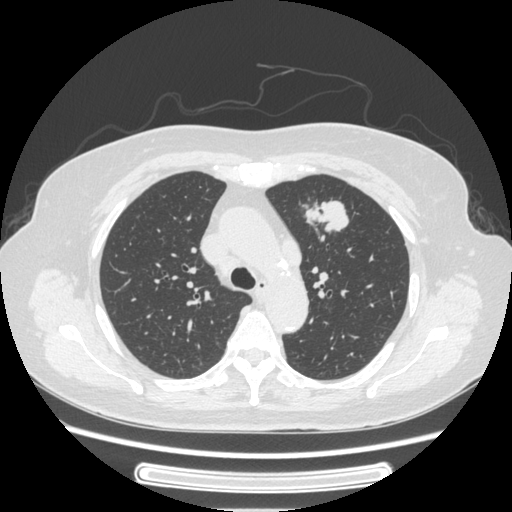
Chest CT, one axial slice. Slice 170 of 227 in the series (ordered by position). Lung window (W 1500 / L -600 HU). 1.25 mm slice thickness. 512 × 512 image matrix, field of view 363 × 363 mm. Patient: female, 77 years. From the clinical record (not read from this slice): clinical TNM (as recorded): T1c N3 M0.
Annotated regions visible in this slice (rectangle marked by the reading radiologist):
- lung tumour (recorded histology: adenocarcinoma): bounding box (x1, y1, x2, y2) in pixels: (304, 192, 360, 247)